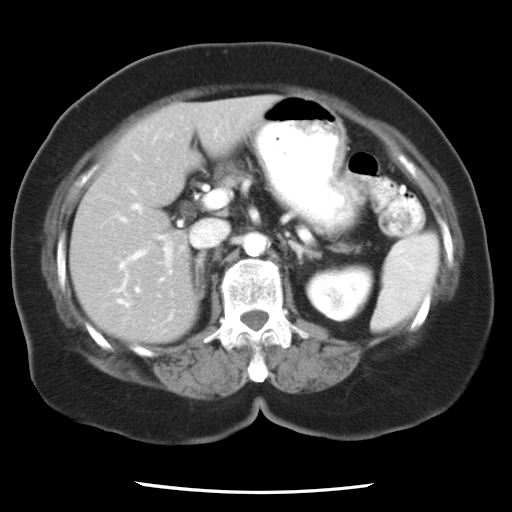
Contrast-enhanced abdominal CT, one axial slice. Slice 12 of 24 in the series (ordered by position). Reconstruction kernel STANDARD. 120 kVp. Intravenous contrast given. Soft-tissue window (W 400 / L 40 HU). 512 × 512 image matrix. Female patient, age 71 years. Case-level facts recorded for this patient, not image findings: diagnosis: colorectal cancer liver metastases, imaged before liver resection; multiple liver metastases: no; largest metastasis: 4.3 cm.
Structures marked on this image (expert manual segmentation):
- hepatic veins: box from (x=119, y=204) to (x=193, y=306) px
- liver: (x=72, y=97)–(x=274, y=341)
- planned liver remnant (the part of the liver to remain after resection): (x=72, y=108)–(x=197, y=341)
- portal vein (with intrahepatic branches): (x=114, y=219)–(x=174, y=296)